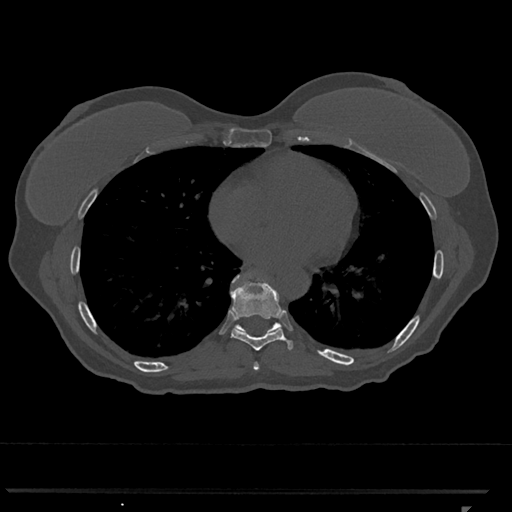
CT including the spine, one axial slice. Position 656 of 793 along the scan axis. 120 kVp. Bone window (W 1800 / L 400 HU). 0.5 mm slice thickness. 512 × 512 image matrix. Female patient, age 62 years. From the clinical record (not read from this slice): primary cancer: renal.
Annotated regions visible in this slice (semi-automatically segmented with operator editing):
- T7 vertebra: bounding box <253,362,259,370> (left, top, right, bottom; pixels)
- T8 vertebra: <230,281,293,351>
- T9 vertebra: <232,274,282,333>